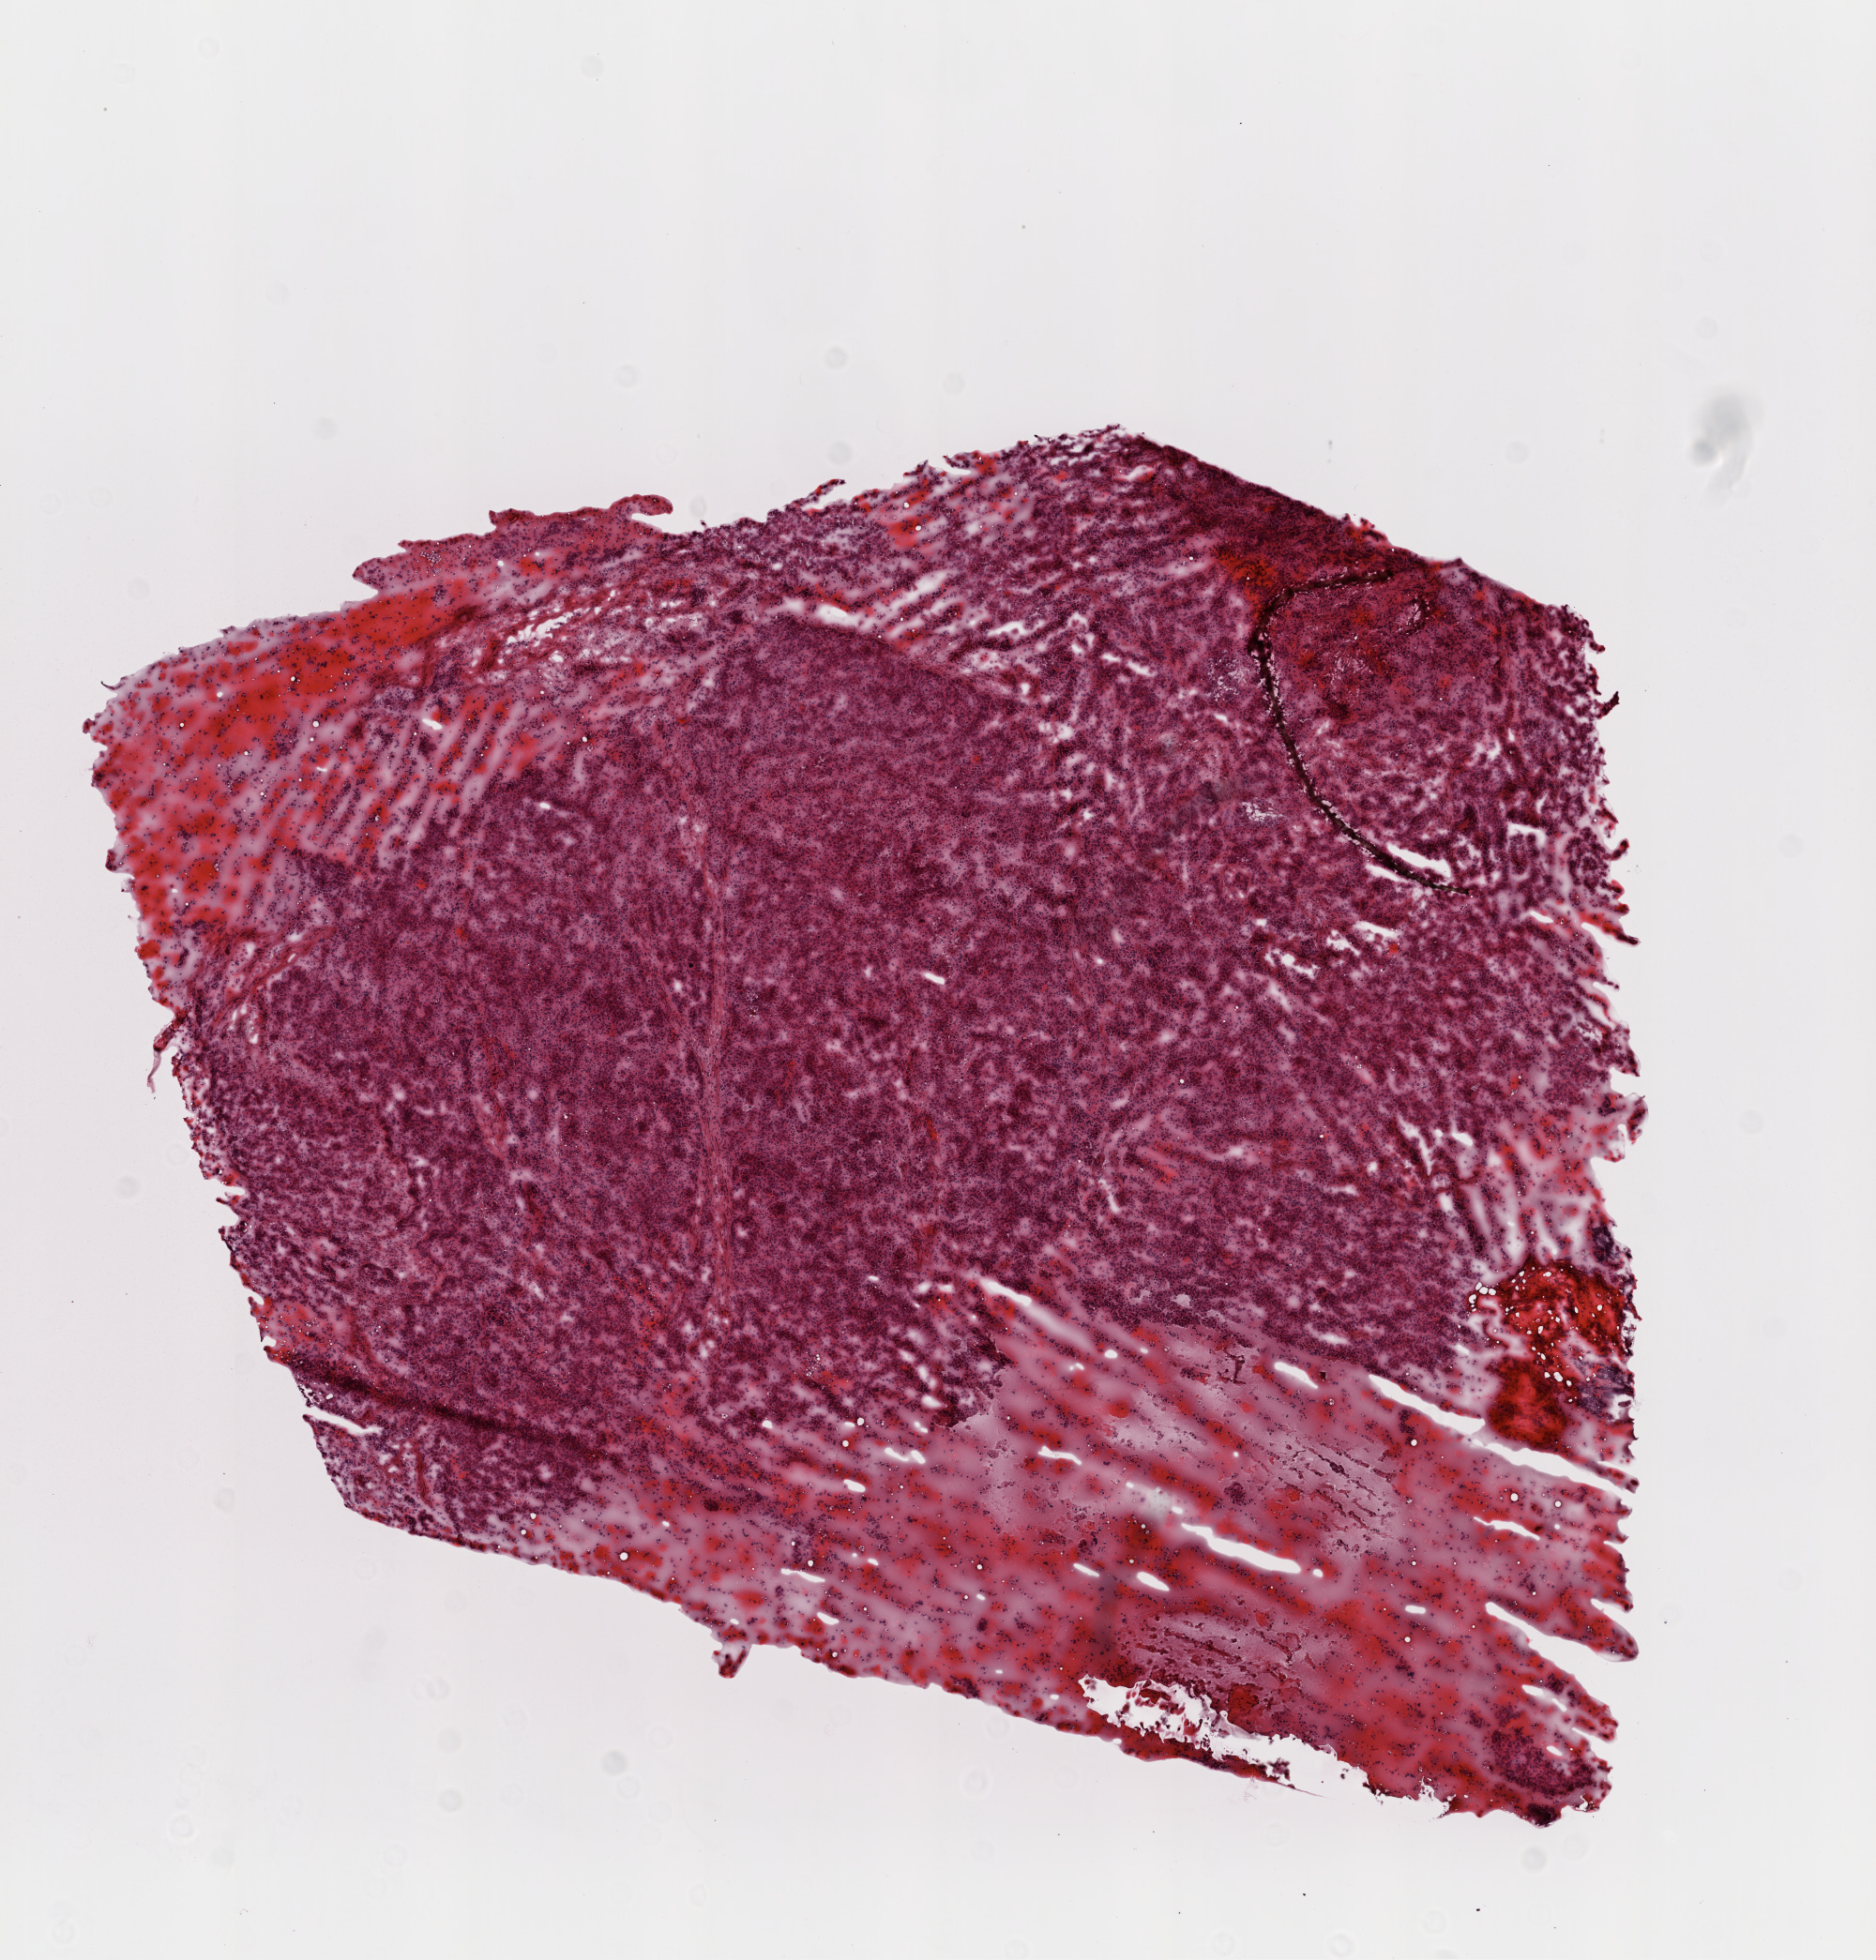
Whole-slide histology image, H&E-stained — whole scanned area (about 8.0 x 8.4 mm) shown as a low-resolution overview; frozen section from the top of the tissue portion; ovary, primary tumour sample. Female patient; age at initial diagnosis 65 years. Histologic grade: G3 (poorly differentiated). Pathologist review of this section (percent, as recorded): tumour cells 70%, tumour nuclei 70%, normal cells 0%, stromal cells 10%, necrosis 20%. Inflammatory infiltration, as recorded: lymphocyte infiltration 0%, monocyte infiltration 0%, neutrophil infiltration 10%.
- pathologic diagnosis: Serous cystadenocarcinoma, NOS
- FIGO stage: IIIC